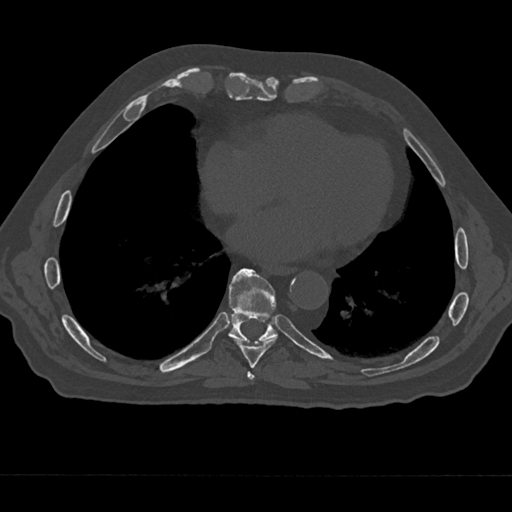
CT including the spine, one axial slice. Position 291 of 797 along the scan axis. Reconstruction kernel Br40s/3. Bone window (W 1800 / L 400 HU). 0.5 mm slice thickness. 512 × 512 image matrix, field of view 377 × 377 mm. Patient: male, 75 years. From the clinical record (not read from this slice): primary cancer: renal; vertebrae with lytic lesions (as recorded): T4.
Outlined on this slice (semi-automatically segmented with operator editing):
- T7 vertebra: bounding box <247,371,255,385> (left, top, right, bottom; pixels)
- T8 vertebra: <233,291,278,368>
- T9 vertebra: <228,268,277,342>